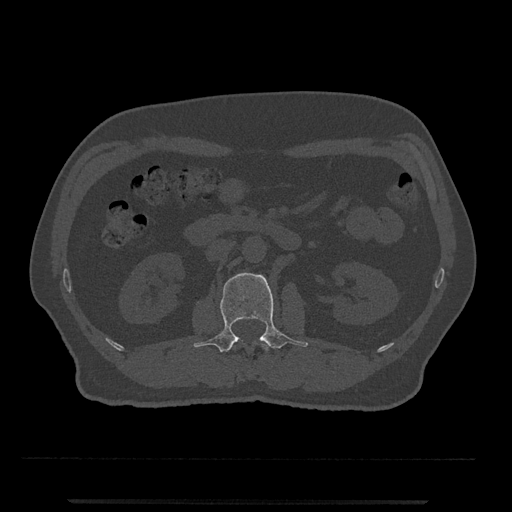
CT including the spine, one axial slice; slice 278 of 797 in the series (ordered by position); reconstruction kernel Br40s/3; bone window (W 1800 / L 400 HU); 0.5 mm slice thickness; 512 × 512 image matrix, field of view 419 × 419 mm. Patient: male, 63 years. Case-level facts recorded for this patient, not image findings: primary cancer: prostate.
Outlined on this slice (semi-automatic segmentation, software-assisted and operator-edited):
- L1 vertebra: bounding box <262,344,268,351> (left, top, right, bottom; pixels)
- L2 vertebra: <193,272,308,352>